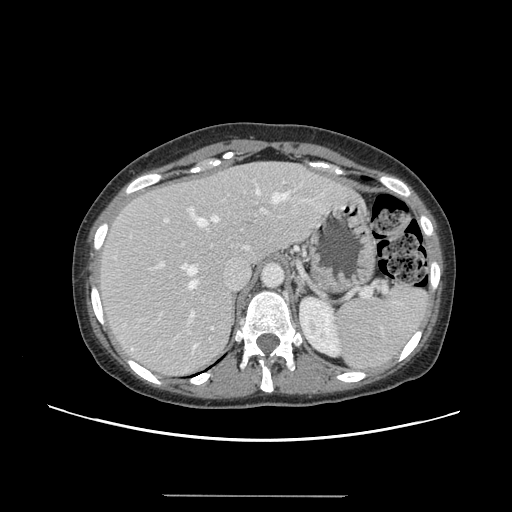
Contrast-enhanced abdominal CT, one axial slice. Slice 104 of 144 in the series (ordered by position). Intravenous contrast given. Soft-tissue window (W 400 / L 40 HU). 512 × 512 image matrix, field of view 380 × 380 mm. Female patient, age 53 years. Case-level facts recorded for this patient, not image findings: diagnosis: colorectal cancer liver metastases, imaged before liver resection.
Structures marked on this image (manually delineated by an expert):
- hepatic veins: bounding box <182,189,288,288> (left, top, right, bottom; pixels)
- liver: <98,162,358,376>
- planned liver remnant (the part of the liver to remain after resection): <98,162,301,301>
- portal vein (with intrahepatic branches): <151,182,284,318>